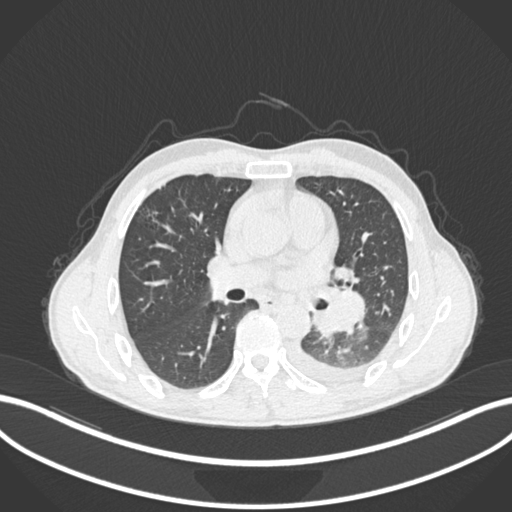
Chest CT, one axial slice. Position 133 of 222 along the scan axis. Reconstruction kernel B30f. 120 kVp. Lung window (W 1500 / L -600 HU). 512 × 512 image matrix, field of view 400 × 400 mm. Patient: male, 47 years. Case-level facts recorded for this patient, not image findings: clinical TNM (as recorded): T3 N1 M1c.
Outlined on this slice (bounding box drawn by a radiologist):
- lung tumour (recorded histology: small cell carcinoma): bounding box <305,286,371,341> (left, top, right, bottom; pixels)